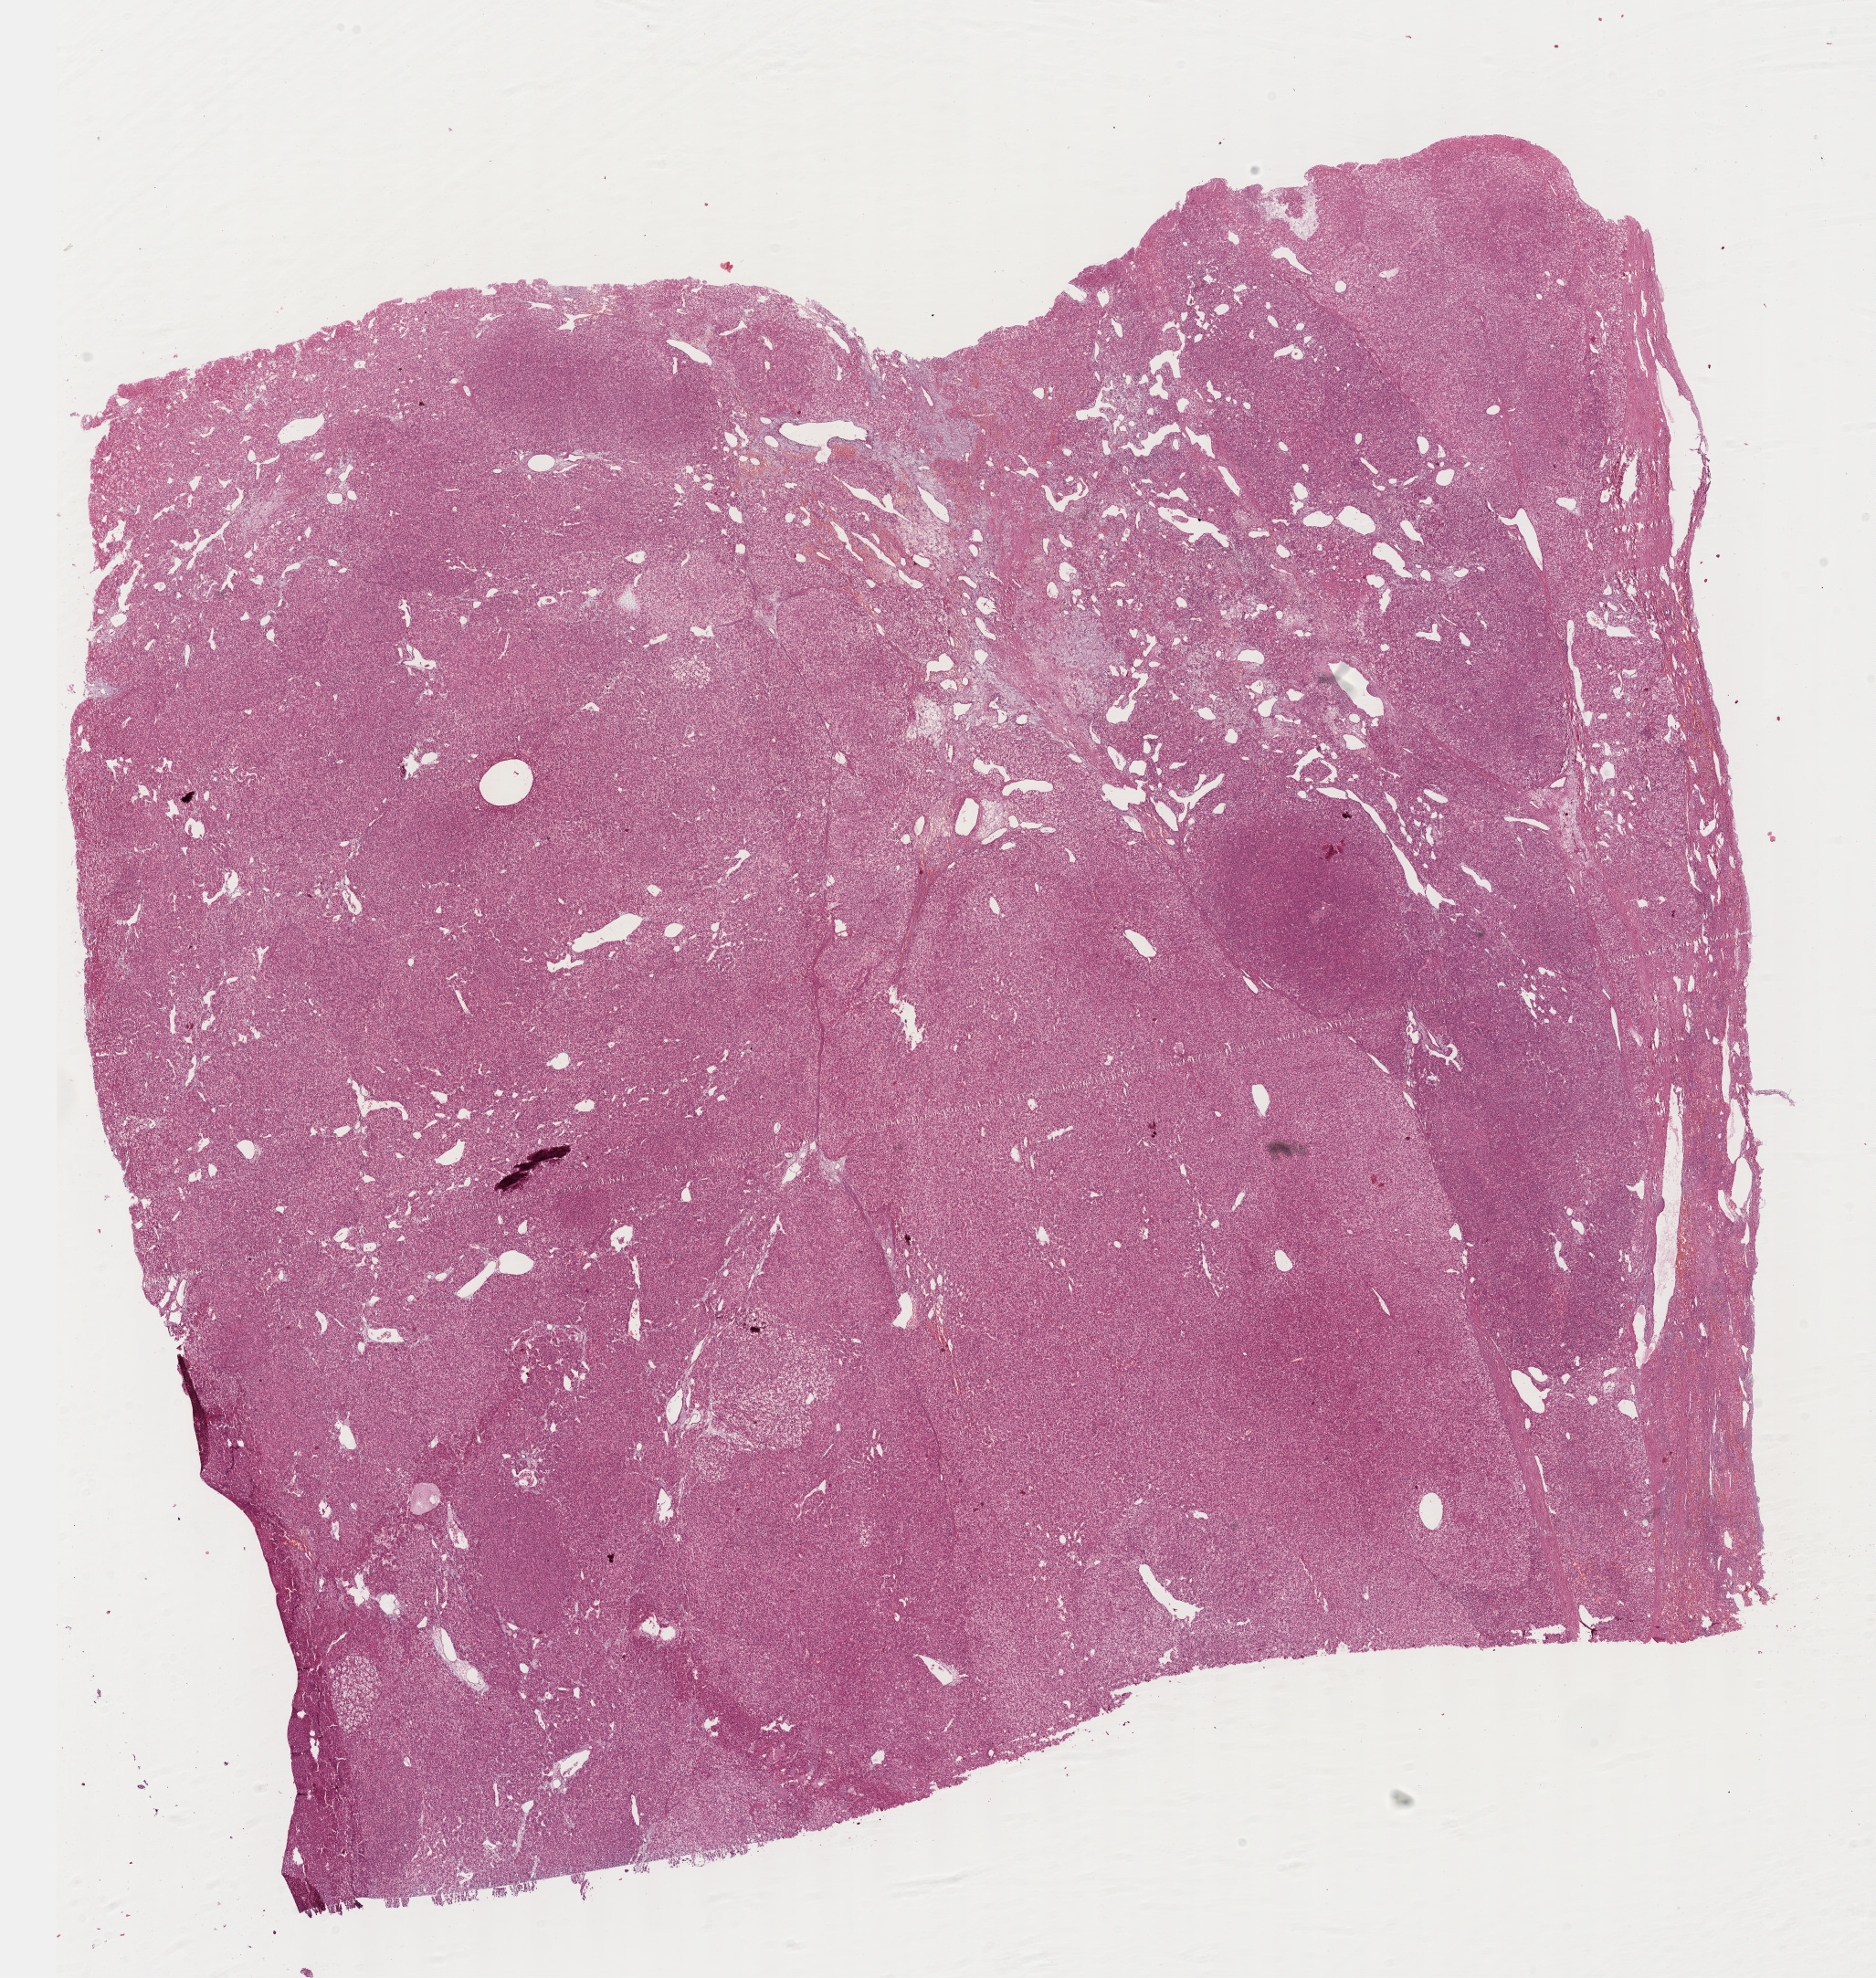
Whole-slide histology image, Hematoxylin and eosin (H&E) stained — a low-resolution overview of the entire scanned area, about 16.6 x 17.5 mm; formalin-fixed paraffin-embedded (FFPE) diagnostic section; sample: primary tumour, liver. Patient: male, age at initial diagnosis 59 years. Histologic grade: G1 (well differentiated).
Diagnosis: Hepatocellular carcinoma, NOS. TNM: T3 N0 M0. AJCC pathologic stage: IIIA (6th edition).